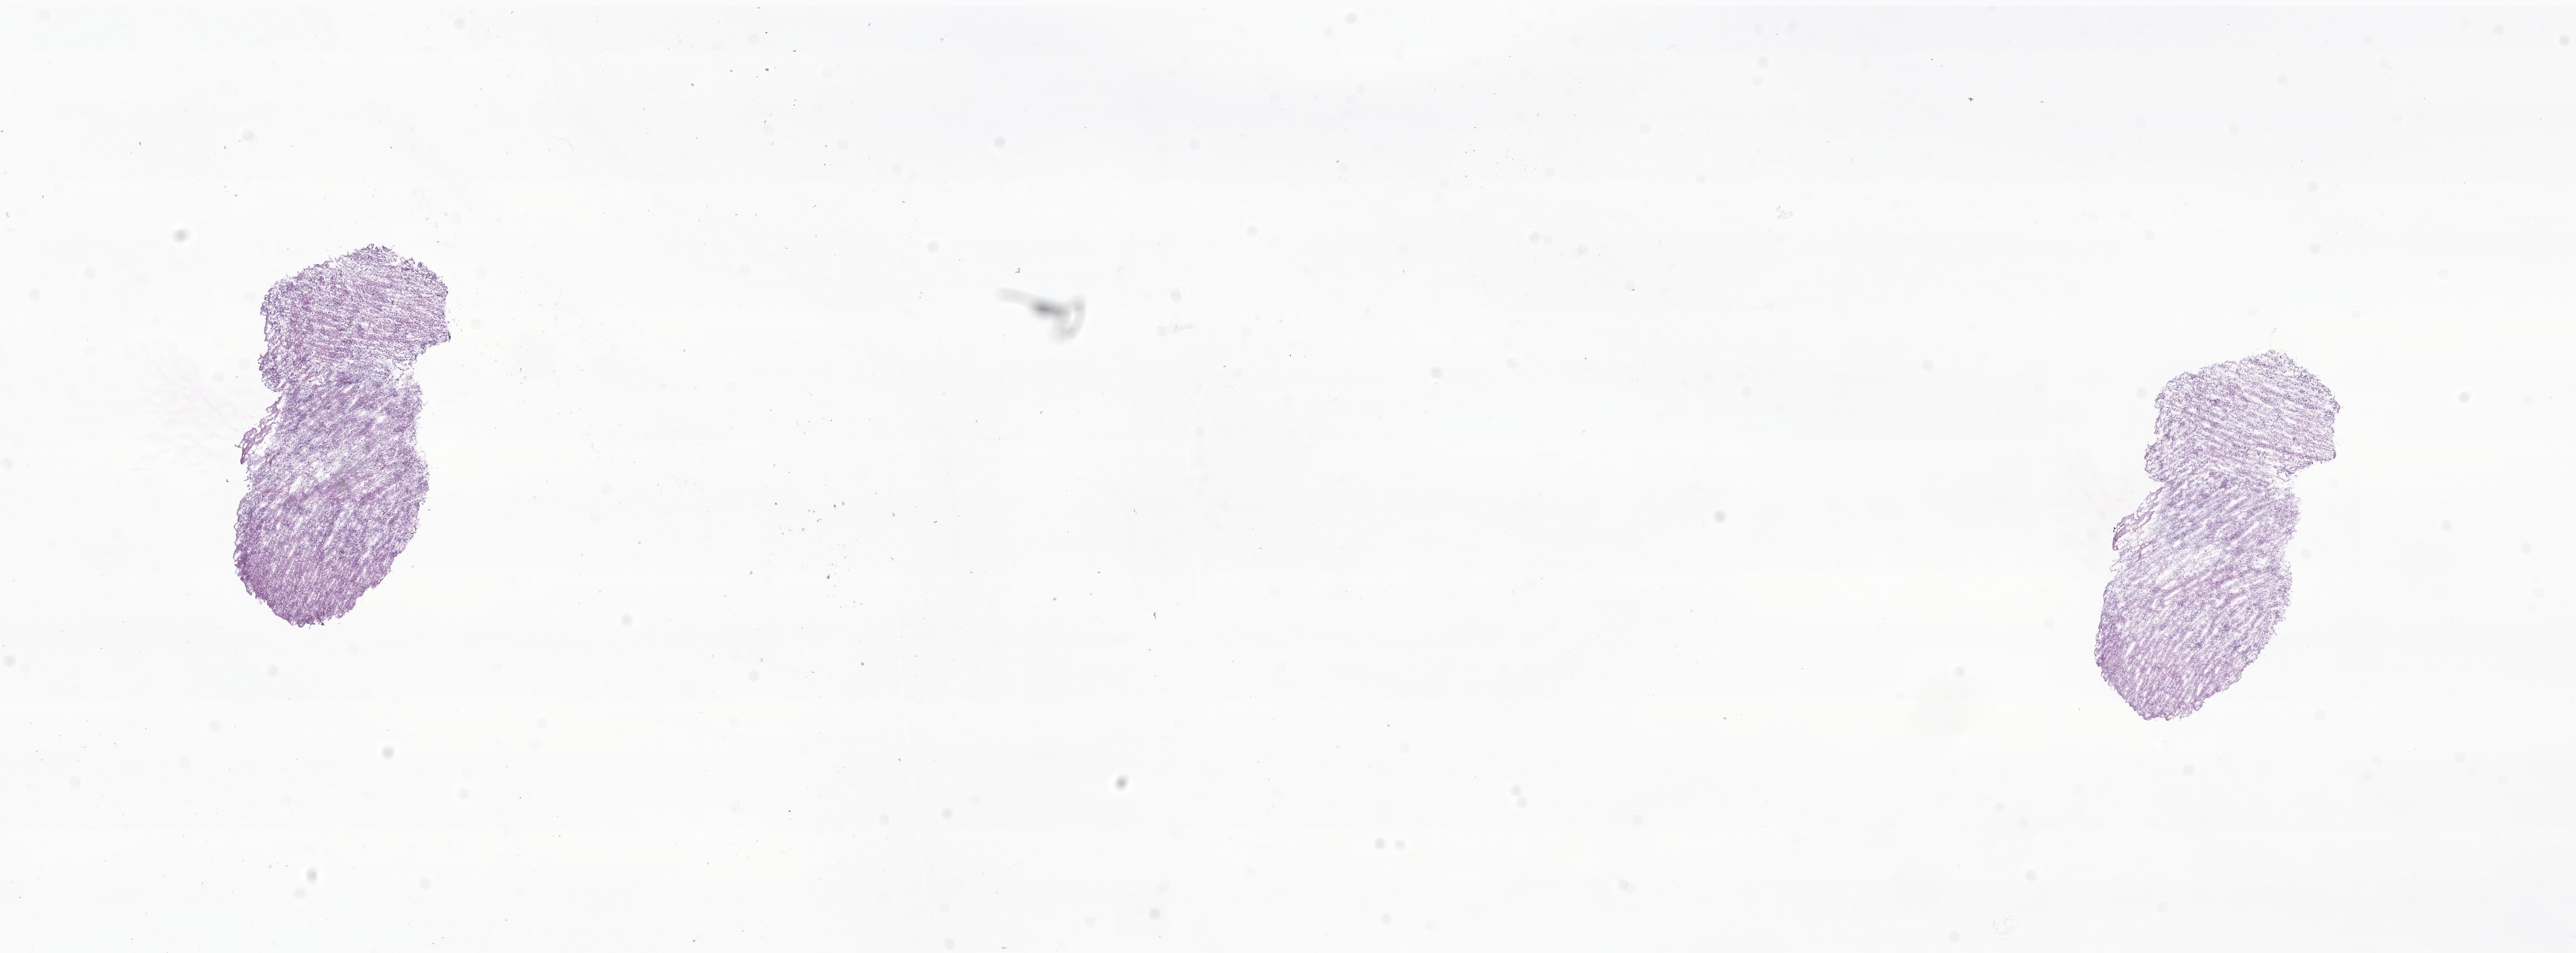
Whole-slide image, haematoxylin and eosin stain of tumor tissue from the brain stem — shown as a low-resolution overview of the whole scanned area (about 21.2 x 7.8 mm); cryosection (OCT / tissue freezing medium). Female patient, age 124 months (10 years 4 months).
* diagnosis: Glioma, malignant